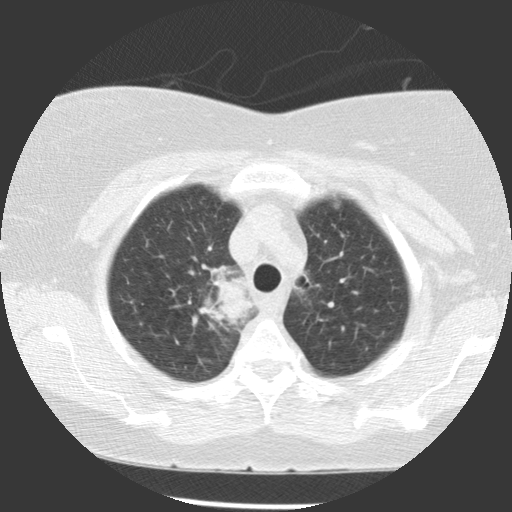
Low-dose screening chest CT, one axial slice. Position 92 of 116 along the scan axis. 140 kVp. Lung window (W 1500 / L -600 HU). 2.5 mm slice thickness. 512 × 512 image matrix, field of view 320 × 320 mm.
Annotated regions visible in this slice (expert manual segmentation):
- lesion 1 (tumor, upper lobe of right lung): bounding box (x1, y1, x2, y2) in pixels: (212, 277, 253, 327)